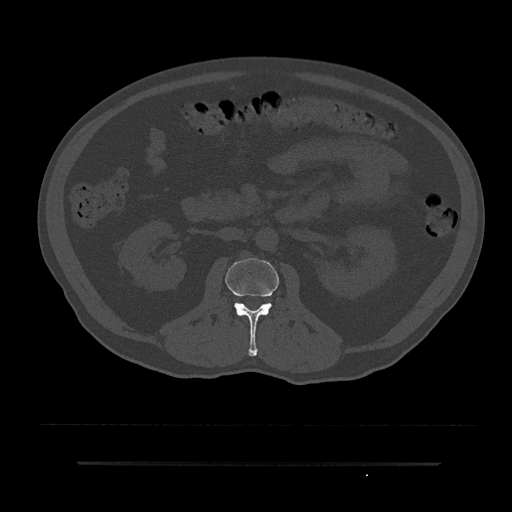
CT including the spine, one axial slice. Position 67 of 797 along the scan axis. Bone window (W 1800 / L 400 HU). 0.5 mm slice thickness. 512 × 512 image matrix, field of view 464 × 464 mm. Male patient, age 59 years. Case-level facts recorded for this patient, not image findings: primary cancer: bile ducts.
Outlined on this slice (semi-automatically segmented with operator editing):
- L2 vertebra: bounding box (x1, y1, x2, y2) in pixels: (225, 258, 279, 356)